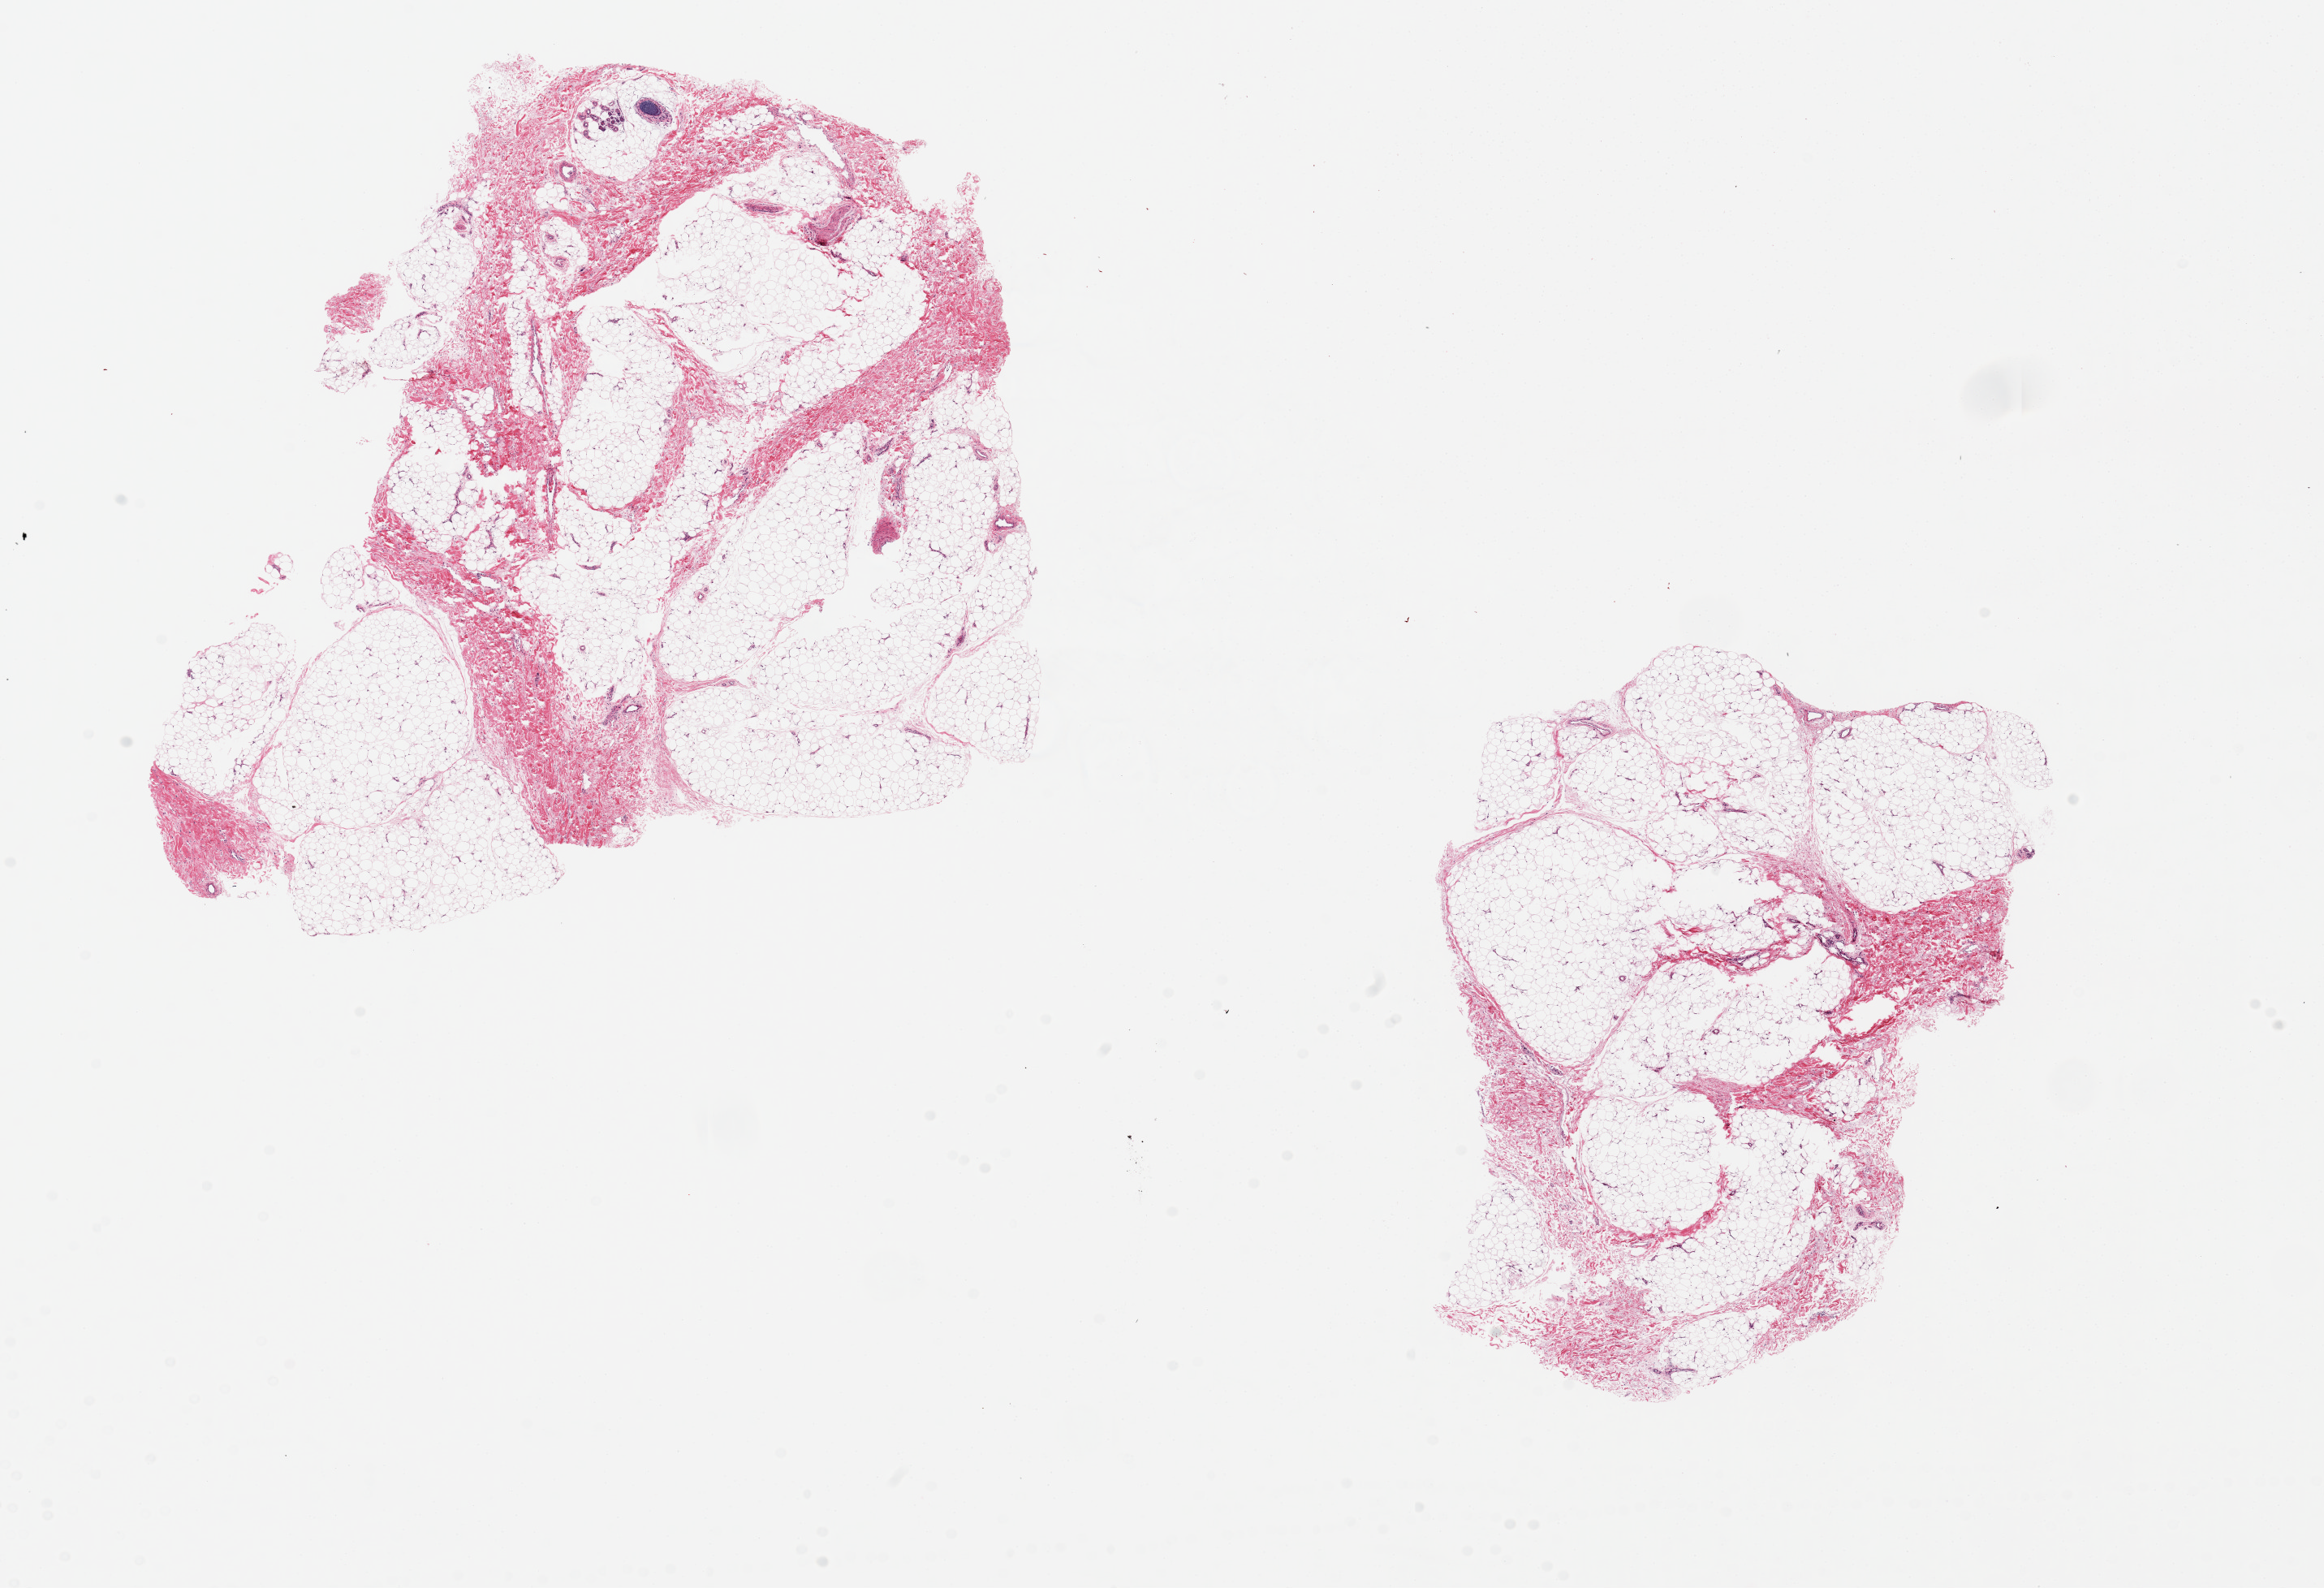
Whole-slide image, hematoxylin and eosin (H&E) stain, brightfield, shown as a low-resolution overview of the whole scanned area (about 22.6 x 15.5 mm, slide scanned at 20x); PAXgene-fixed paraffin-embedded (PFPE) section; sampled site (target tissue): adipose tissue; donor tissue sample. Donor: male.
• reviewer comment on this tissue sample: 2 pieces, 8x8 & 8x6mm; Fibroadipose tissue (~30% fibrous stroma admixed); no fixation or traumatic artifacts